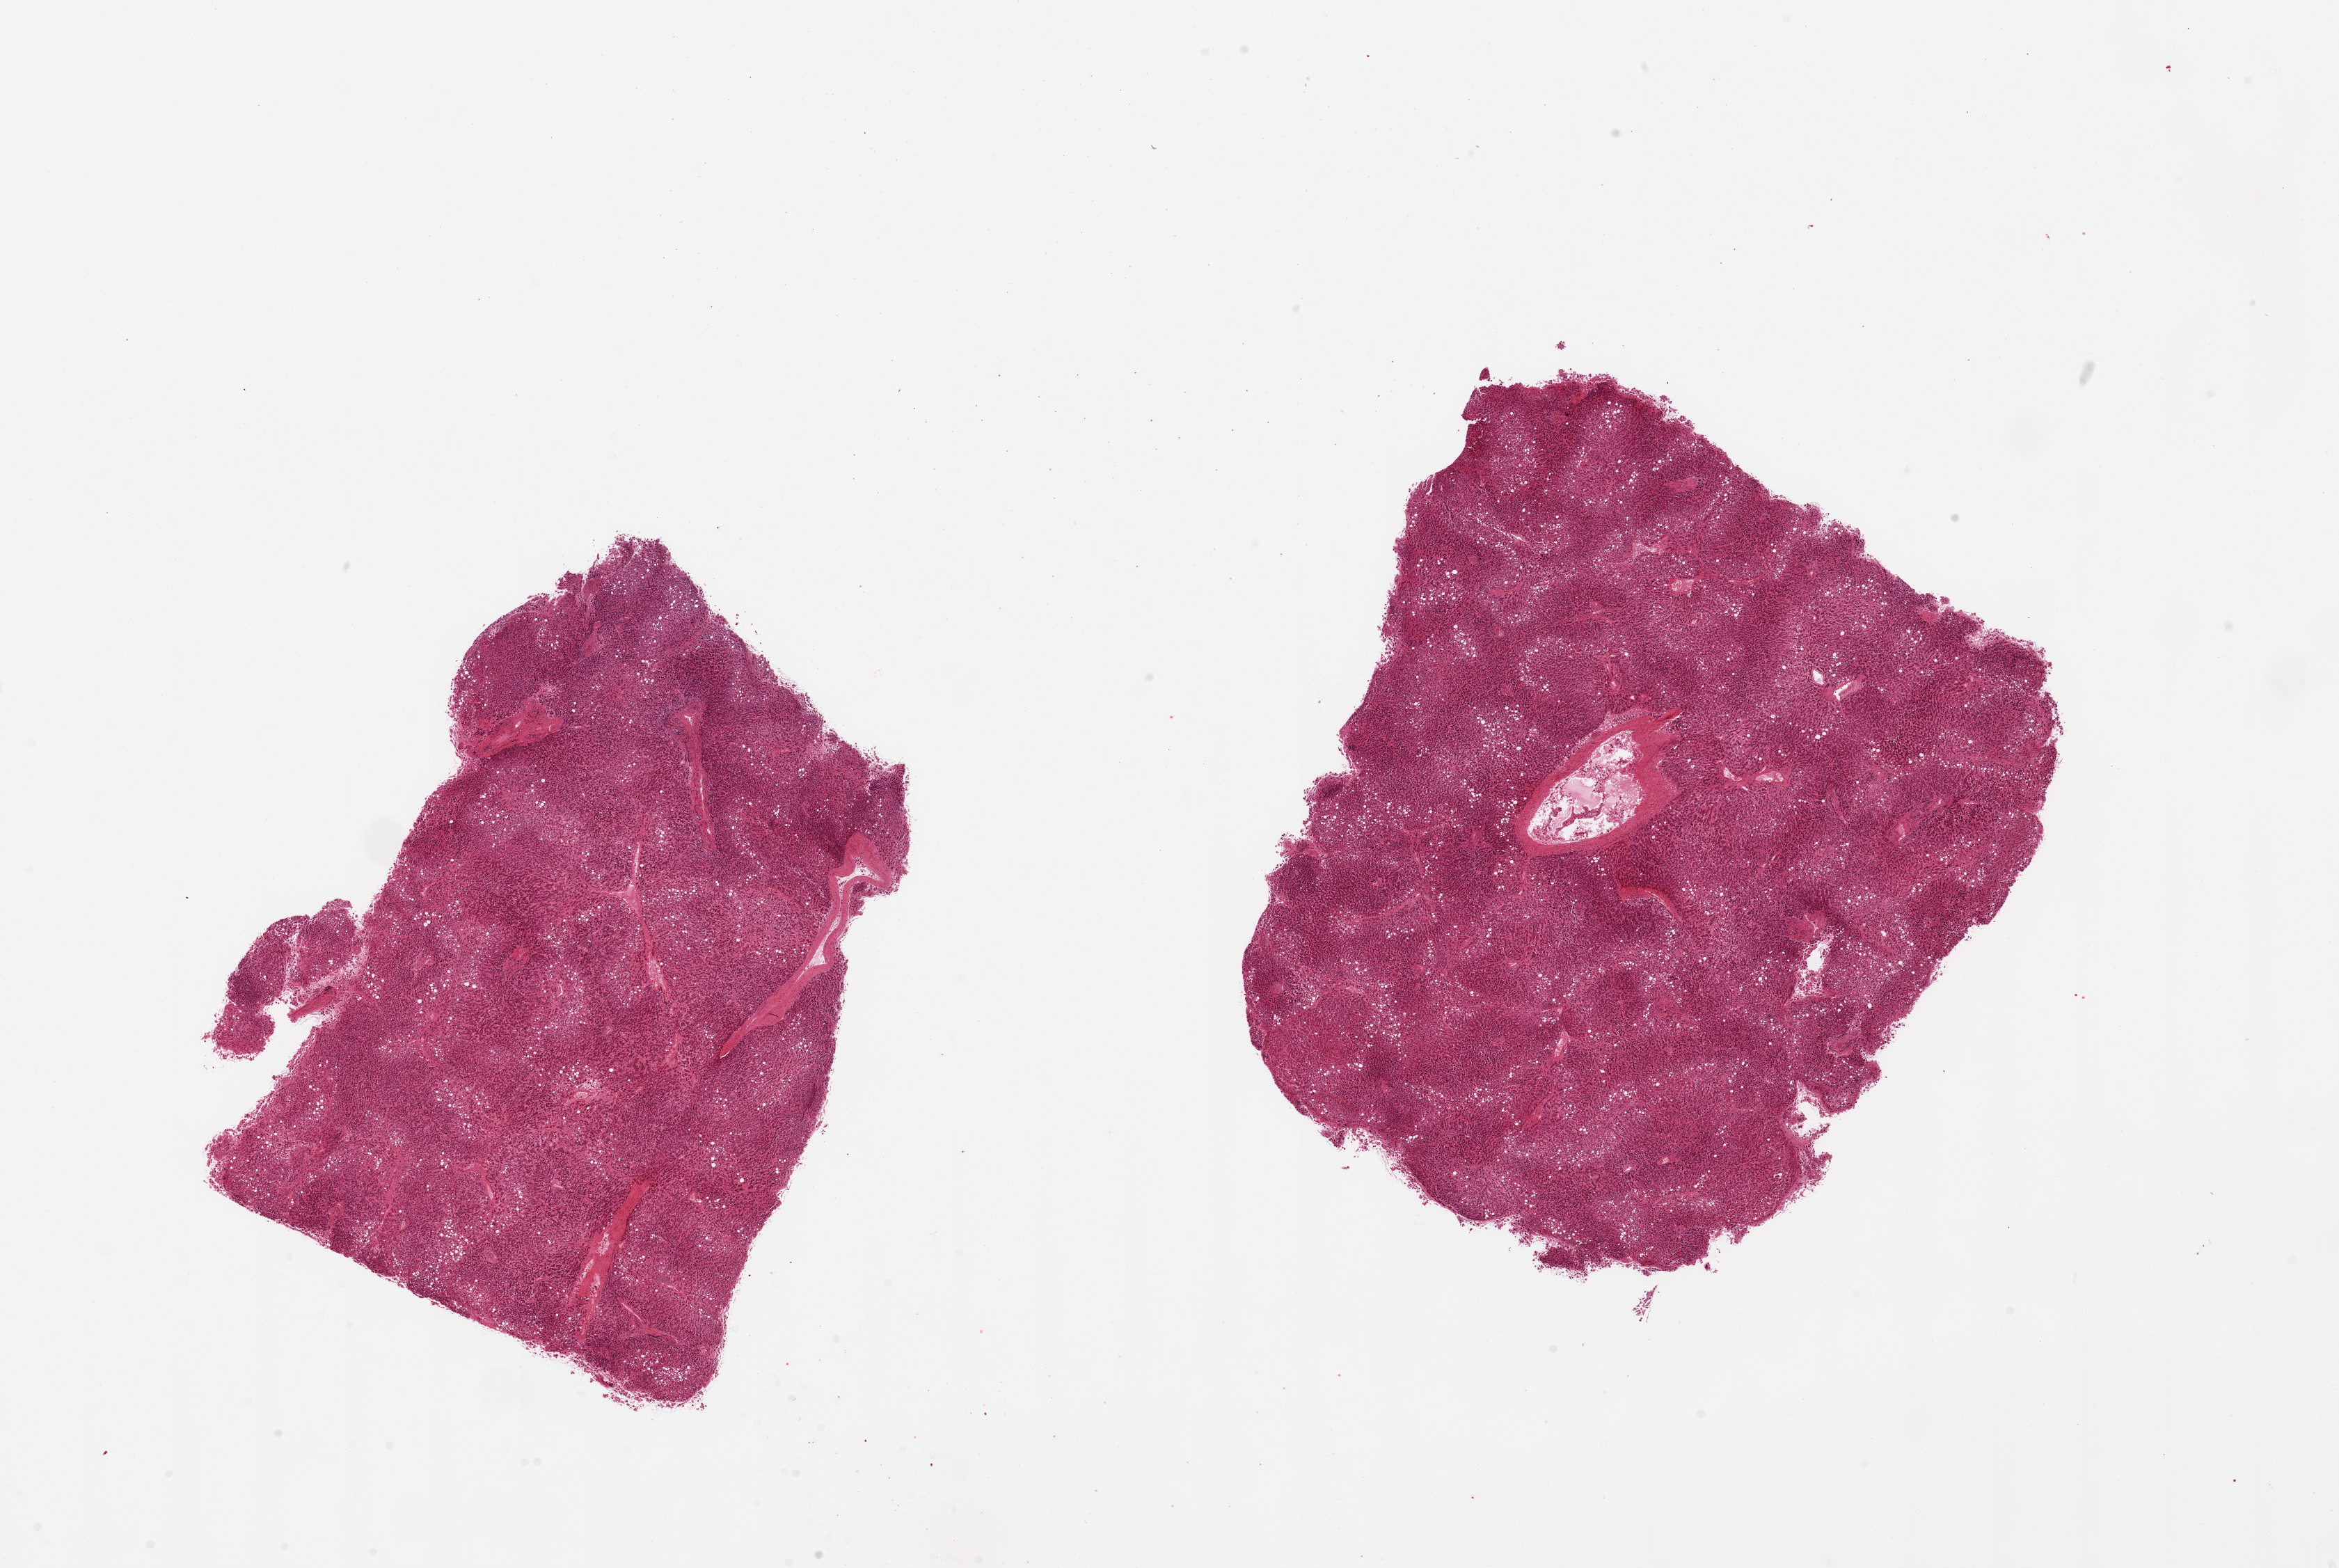
Whole-slide image, H&E stain, whole scanned area (about 26.6 x 17.8 mm) shown as a low-resolution overview. PAXgene-fixed paraffin-embedded (PFPE) section. Target tissue: liver. Tissue donor sample. Male donor.
* reviewer comment on this tissue sample: 2 pieces; congestion and steatosis